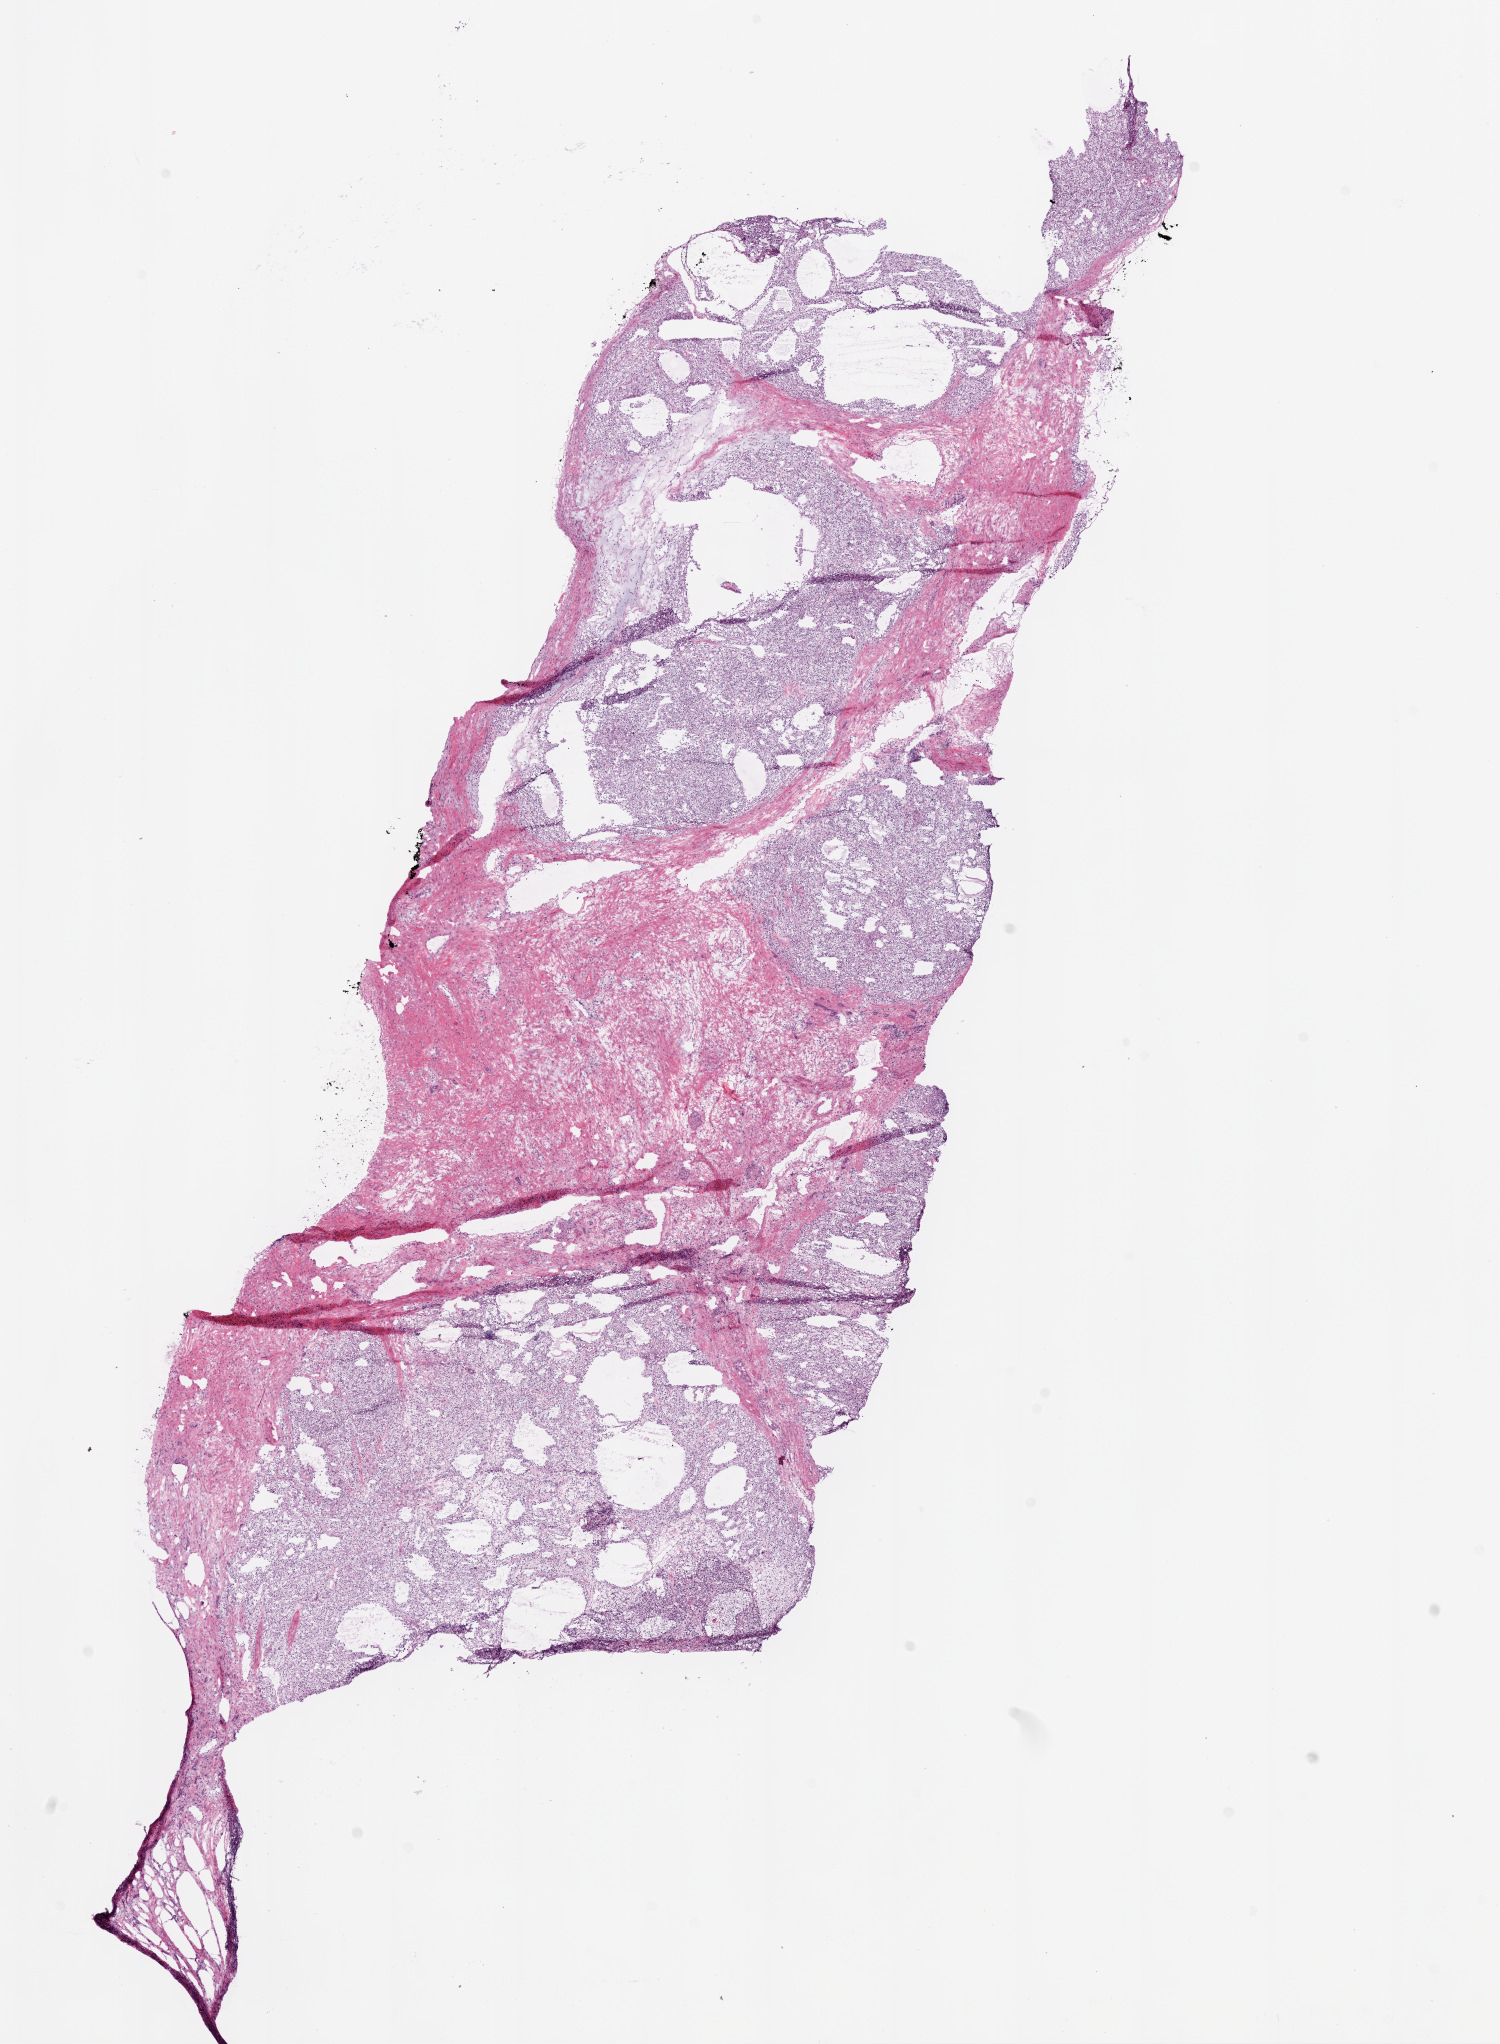
Whole-slide histology image, H&E — a low-resolution overview of the entire scanned area, about 12.0 x 16.4 mm. Frozen section. Primary tumour sample from the kidney. Male patient; age at initial diagnosis 51 years. Histologic grade: G2 (moderately differentiated). Composition of this section per pathologist review: tumour cells 65%, tumour nuclei 80%, normal cells 30%, stromal cells 5%, necrosis 0%.
AJCC pathologic stage: I. Laterality: left. Pathologic diagnosis: Clear cell adenocarcinoma, NOS.